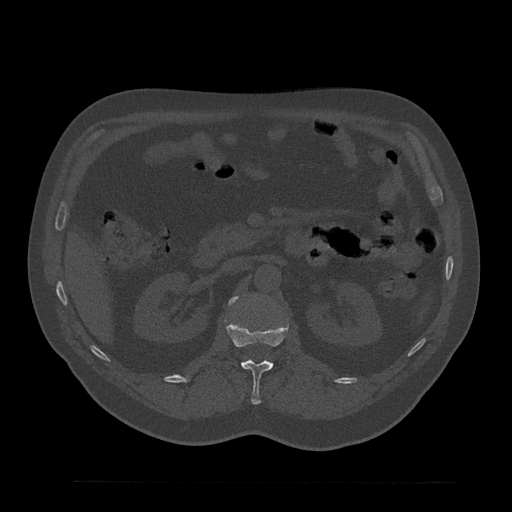
CT including the spine, one axial slice; slice 151 of 797 in the series (ordered by position); reconstruction kernel Br40s/3; 120 kVp; bone window (W 1800 / L 400 HU); 0.5 mm slice thickness; 512 × 512 image matrix, field of view 430 × 430 mm. Male patient, age 61 years. Case-level facts recorded for this patient, not image findings: primary cancer: prostate.
Outlined on this slice (semi-automatically segmented with operator editing):
- L1 vertebra: bounding box (x1, y1, x2, y2) in pixels: (225, 320, 288, 405)
- L2 vertebra: (229, 297, 237, 304)